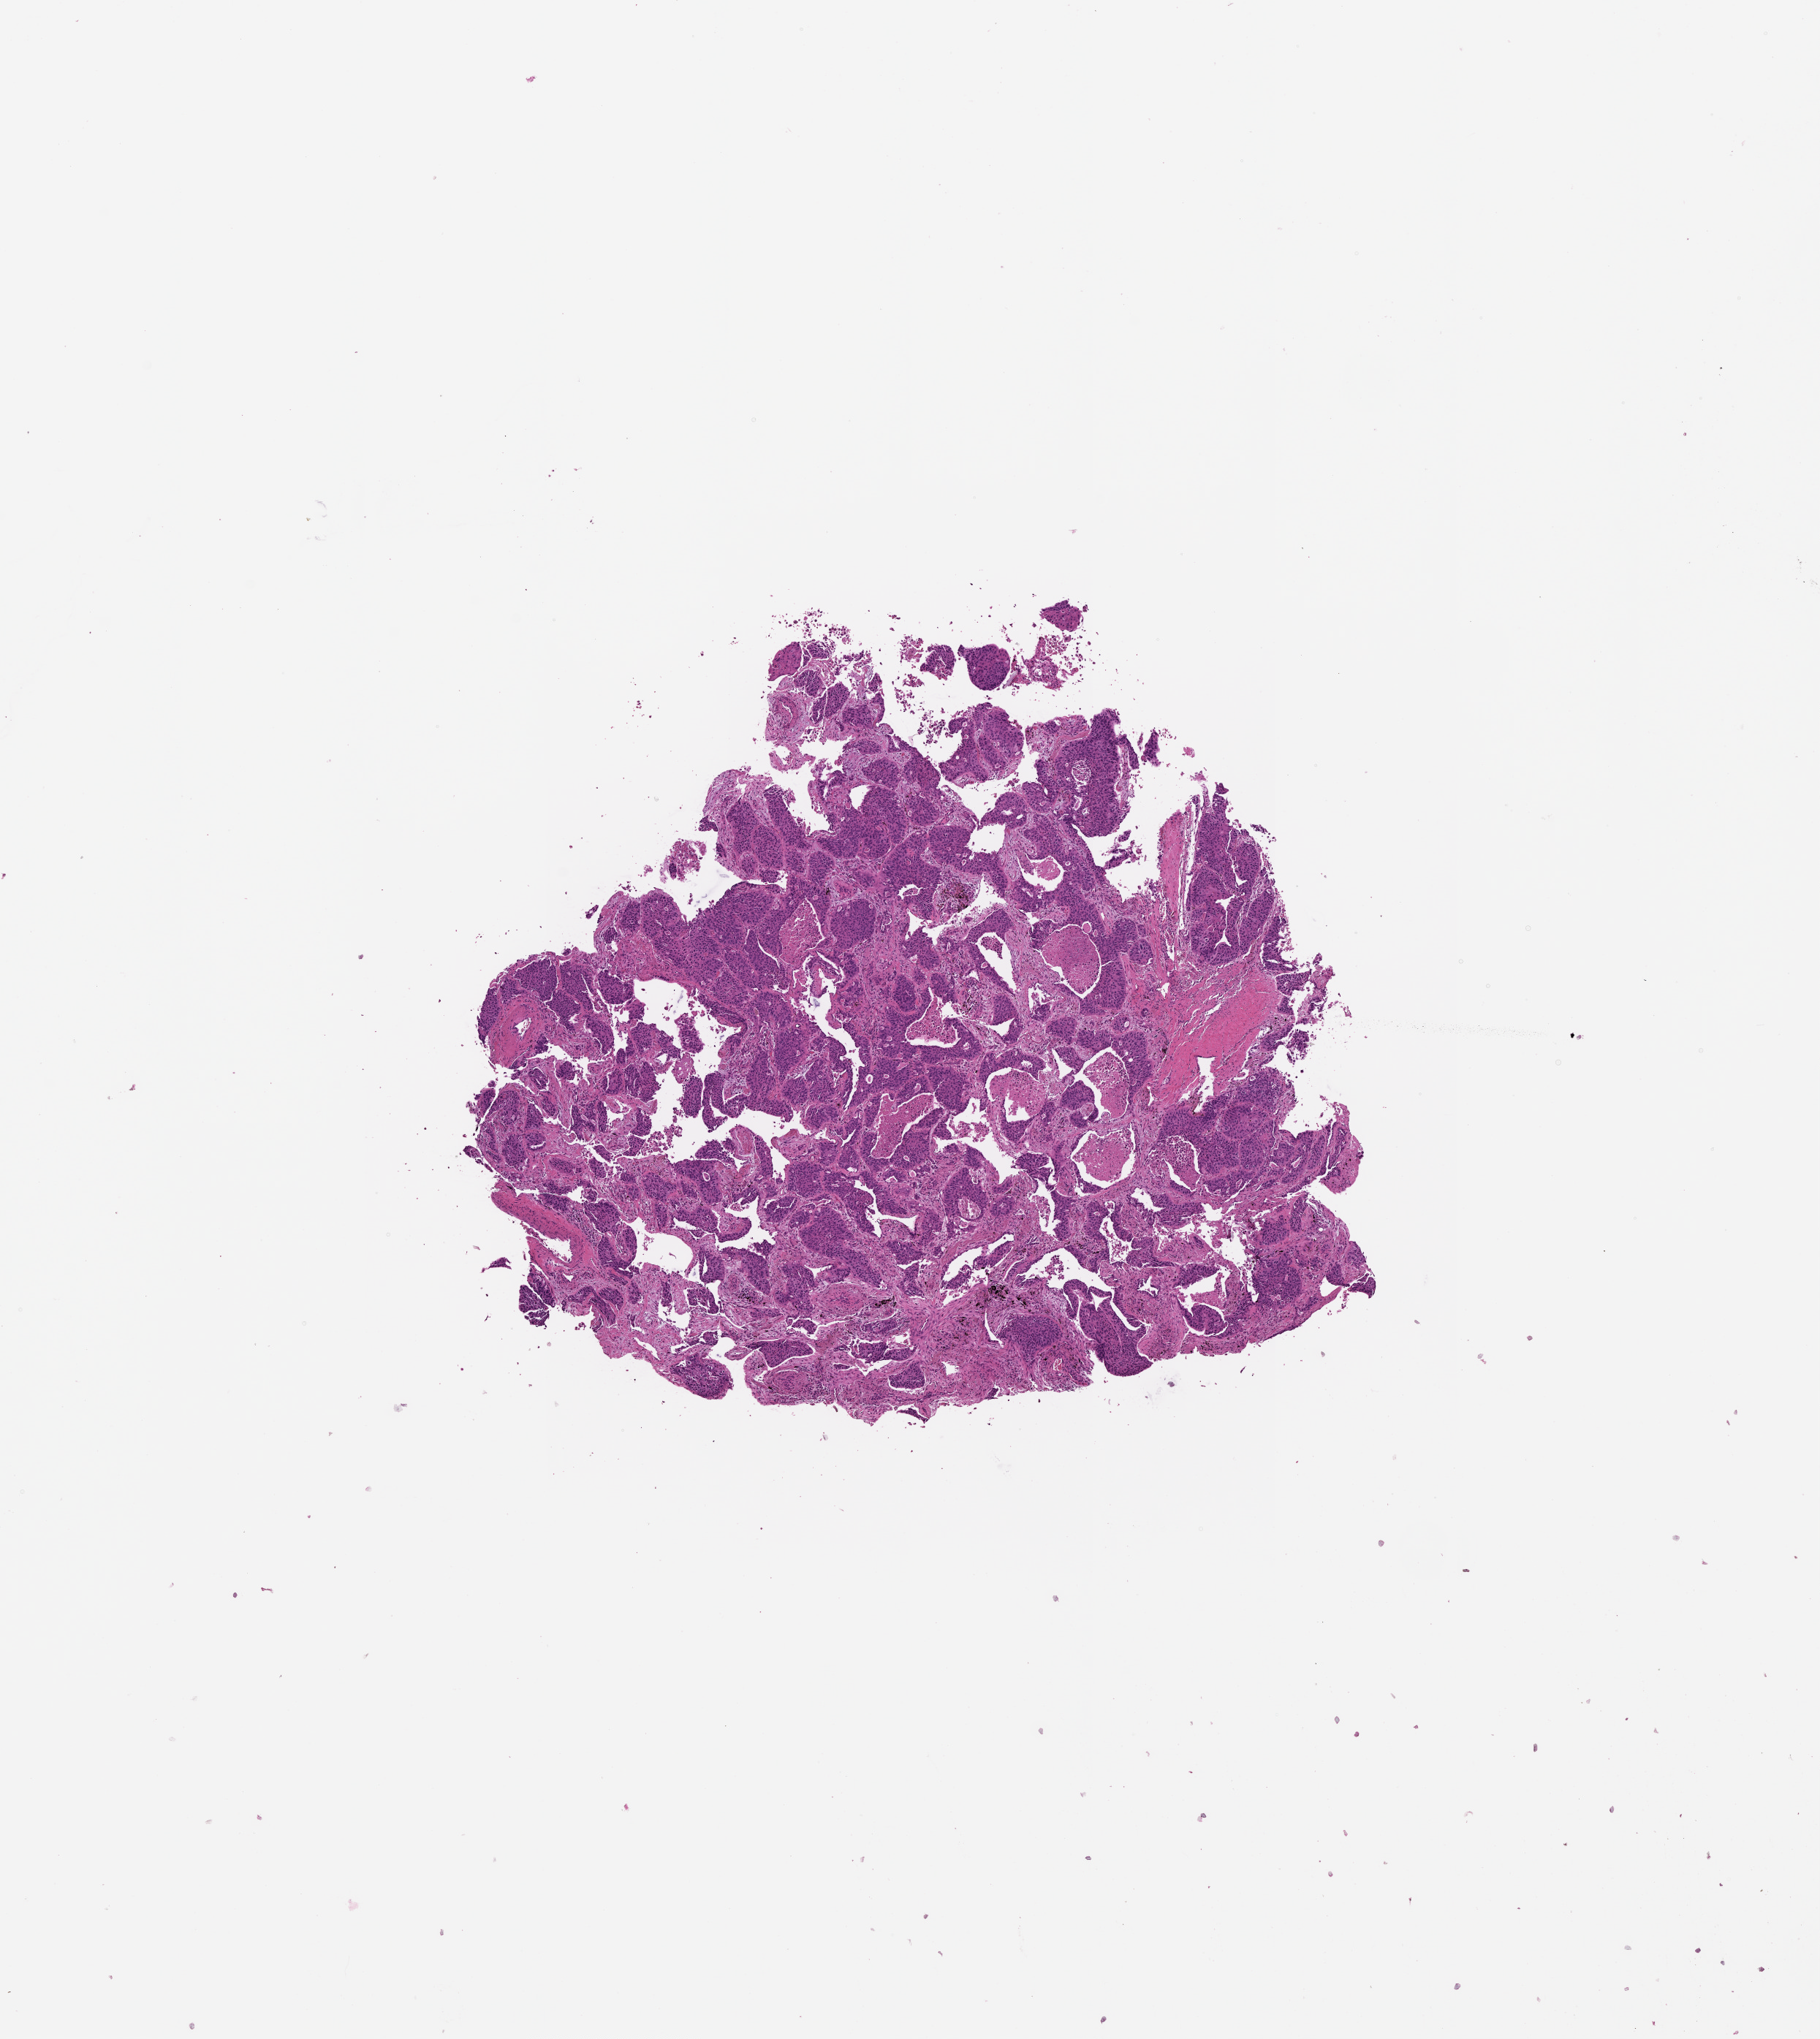
Whole-slide histology image, H&E — a low-resolution overview of the entire scanned area, about 10.0 x 11.2 mm. Lung, tissue type not recorded.
Patient diagnosis (cohort enrolment): squamous cell carcinoma (lung).